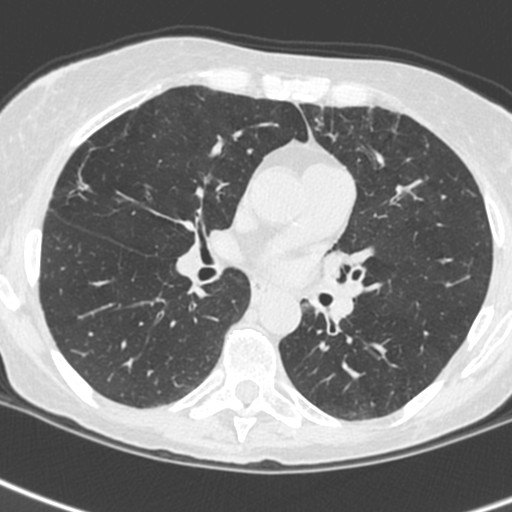
Low-dose screening chest CT, one axial slice. Slice 135 of 242 in the series (ordered by position). 120 kVp. Lung window (W 1500 / L -600 HU). 1.3 mm slice thickness. 512 × 512 image matrix, field of view 284 × 284 mm.
Structures marked on this image (manually delineated by an expert):
- lesion 3 (tumor, upper lobe of left lung): bounding box (x1, y1, x2, y2) in pixels: (307, 252, 362, 323)